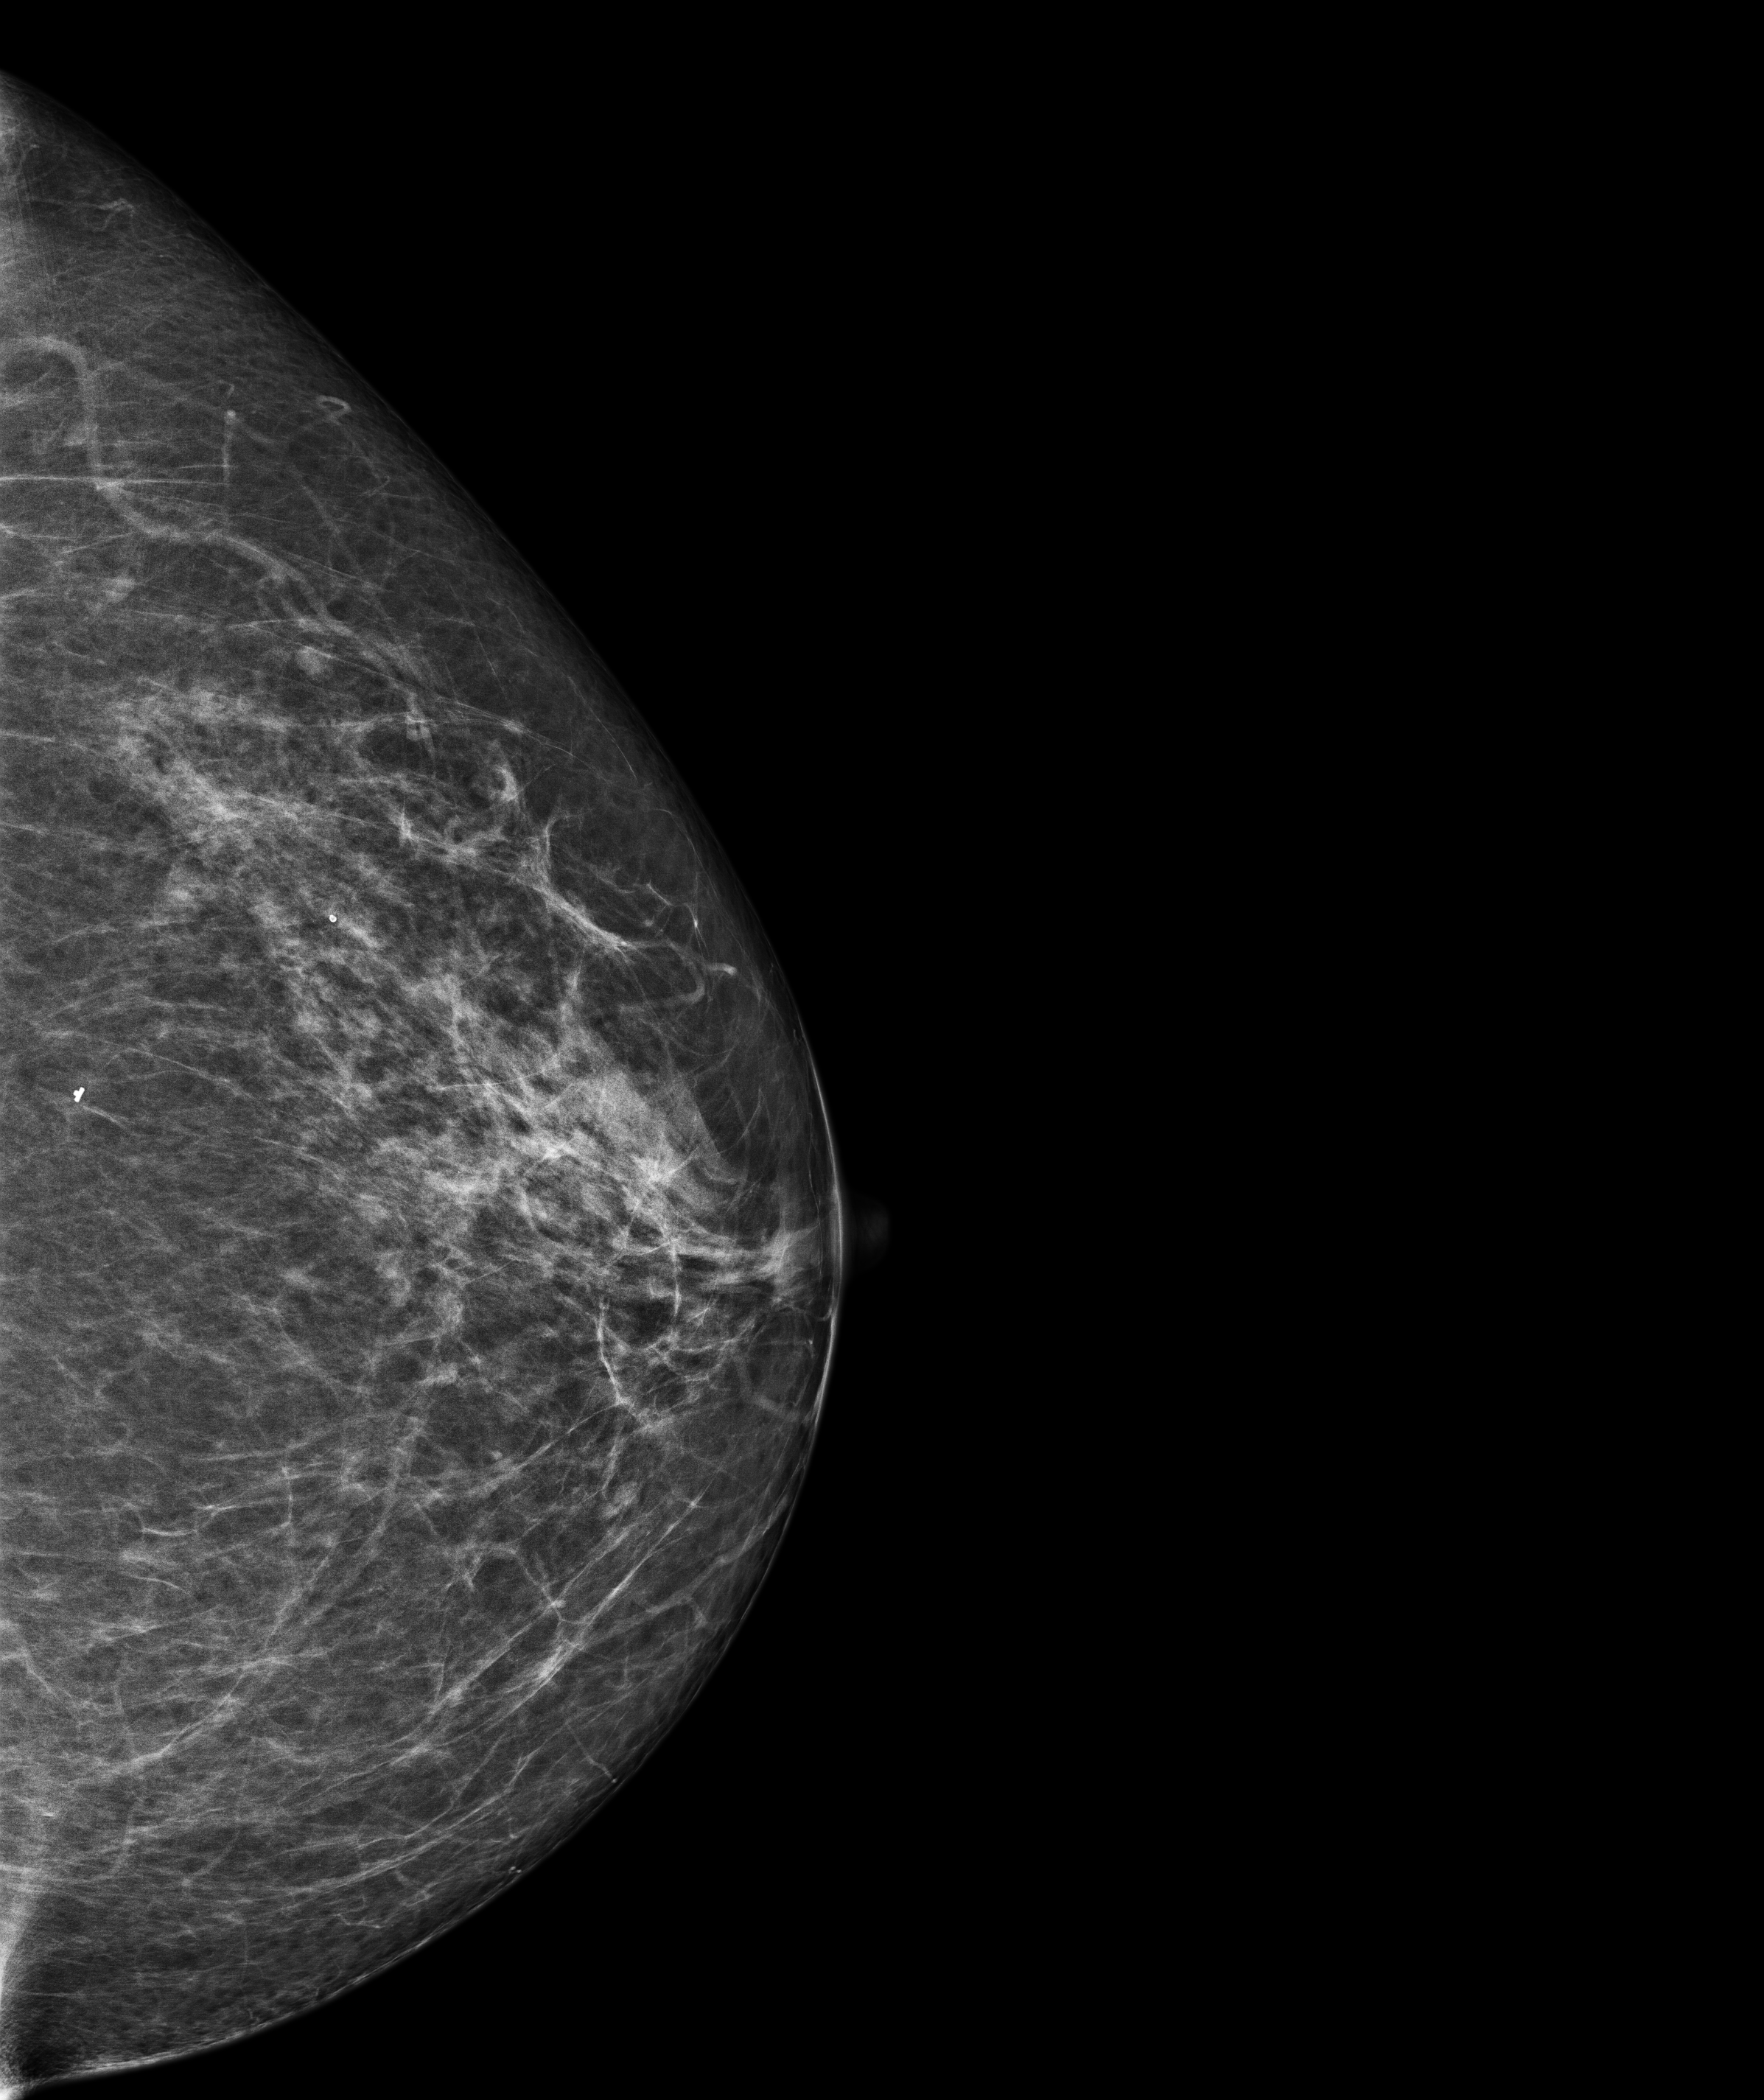
Screening examination, compressed breast thickness 73.7 mm. Female patient, age 54 years.
Image type: full-field digital mammogram. Breast: left. Projection: craniocaudal (CC) view.